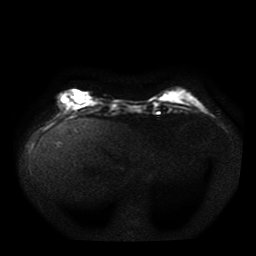
Breast MRI, one axial slice; slice 11 of 41 in the series (ordered by position); diffusion-weighted series; image 2 of 4 stored at this slice position (different b-values; order by instance number); 1.5 T; 5 mm slice thickness; 256 × 256 image matrix. Female patient.
Annotated regions visible in this slice (outlined manually by an expert reader):
- tumour on diffusion-weighted imaging: bounding box <61,93,91,108> (left, top, right, bottom; pixels)